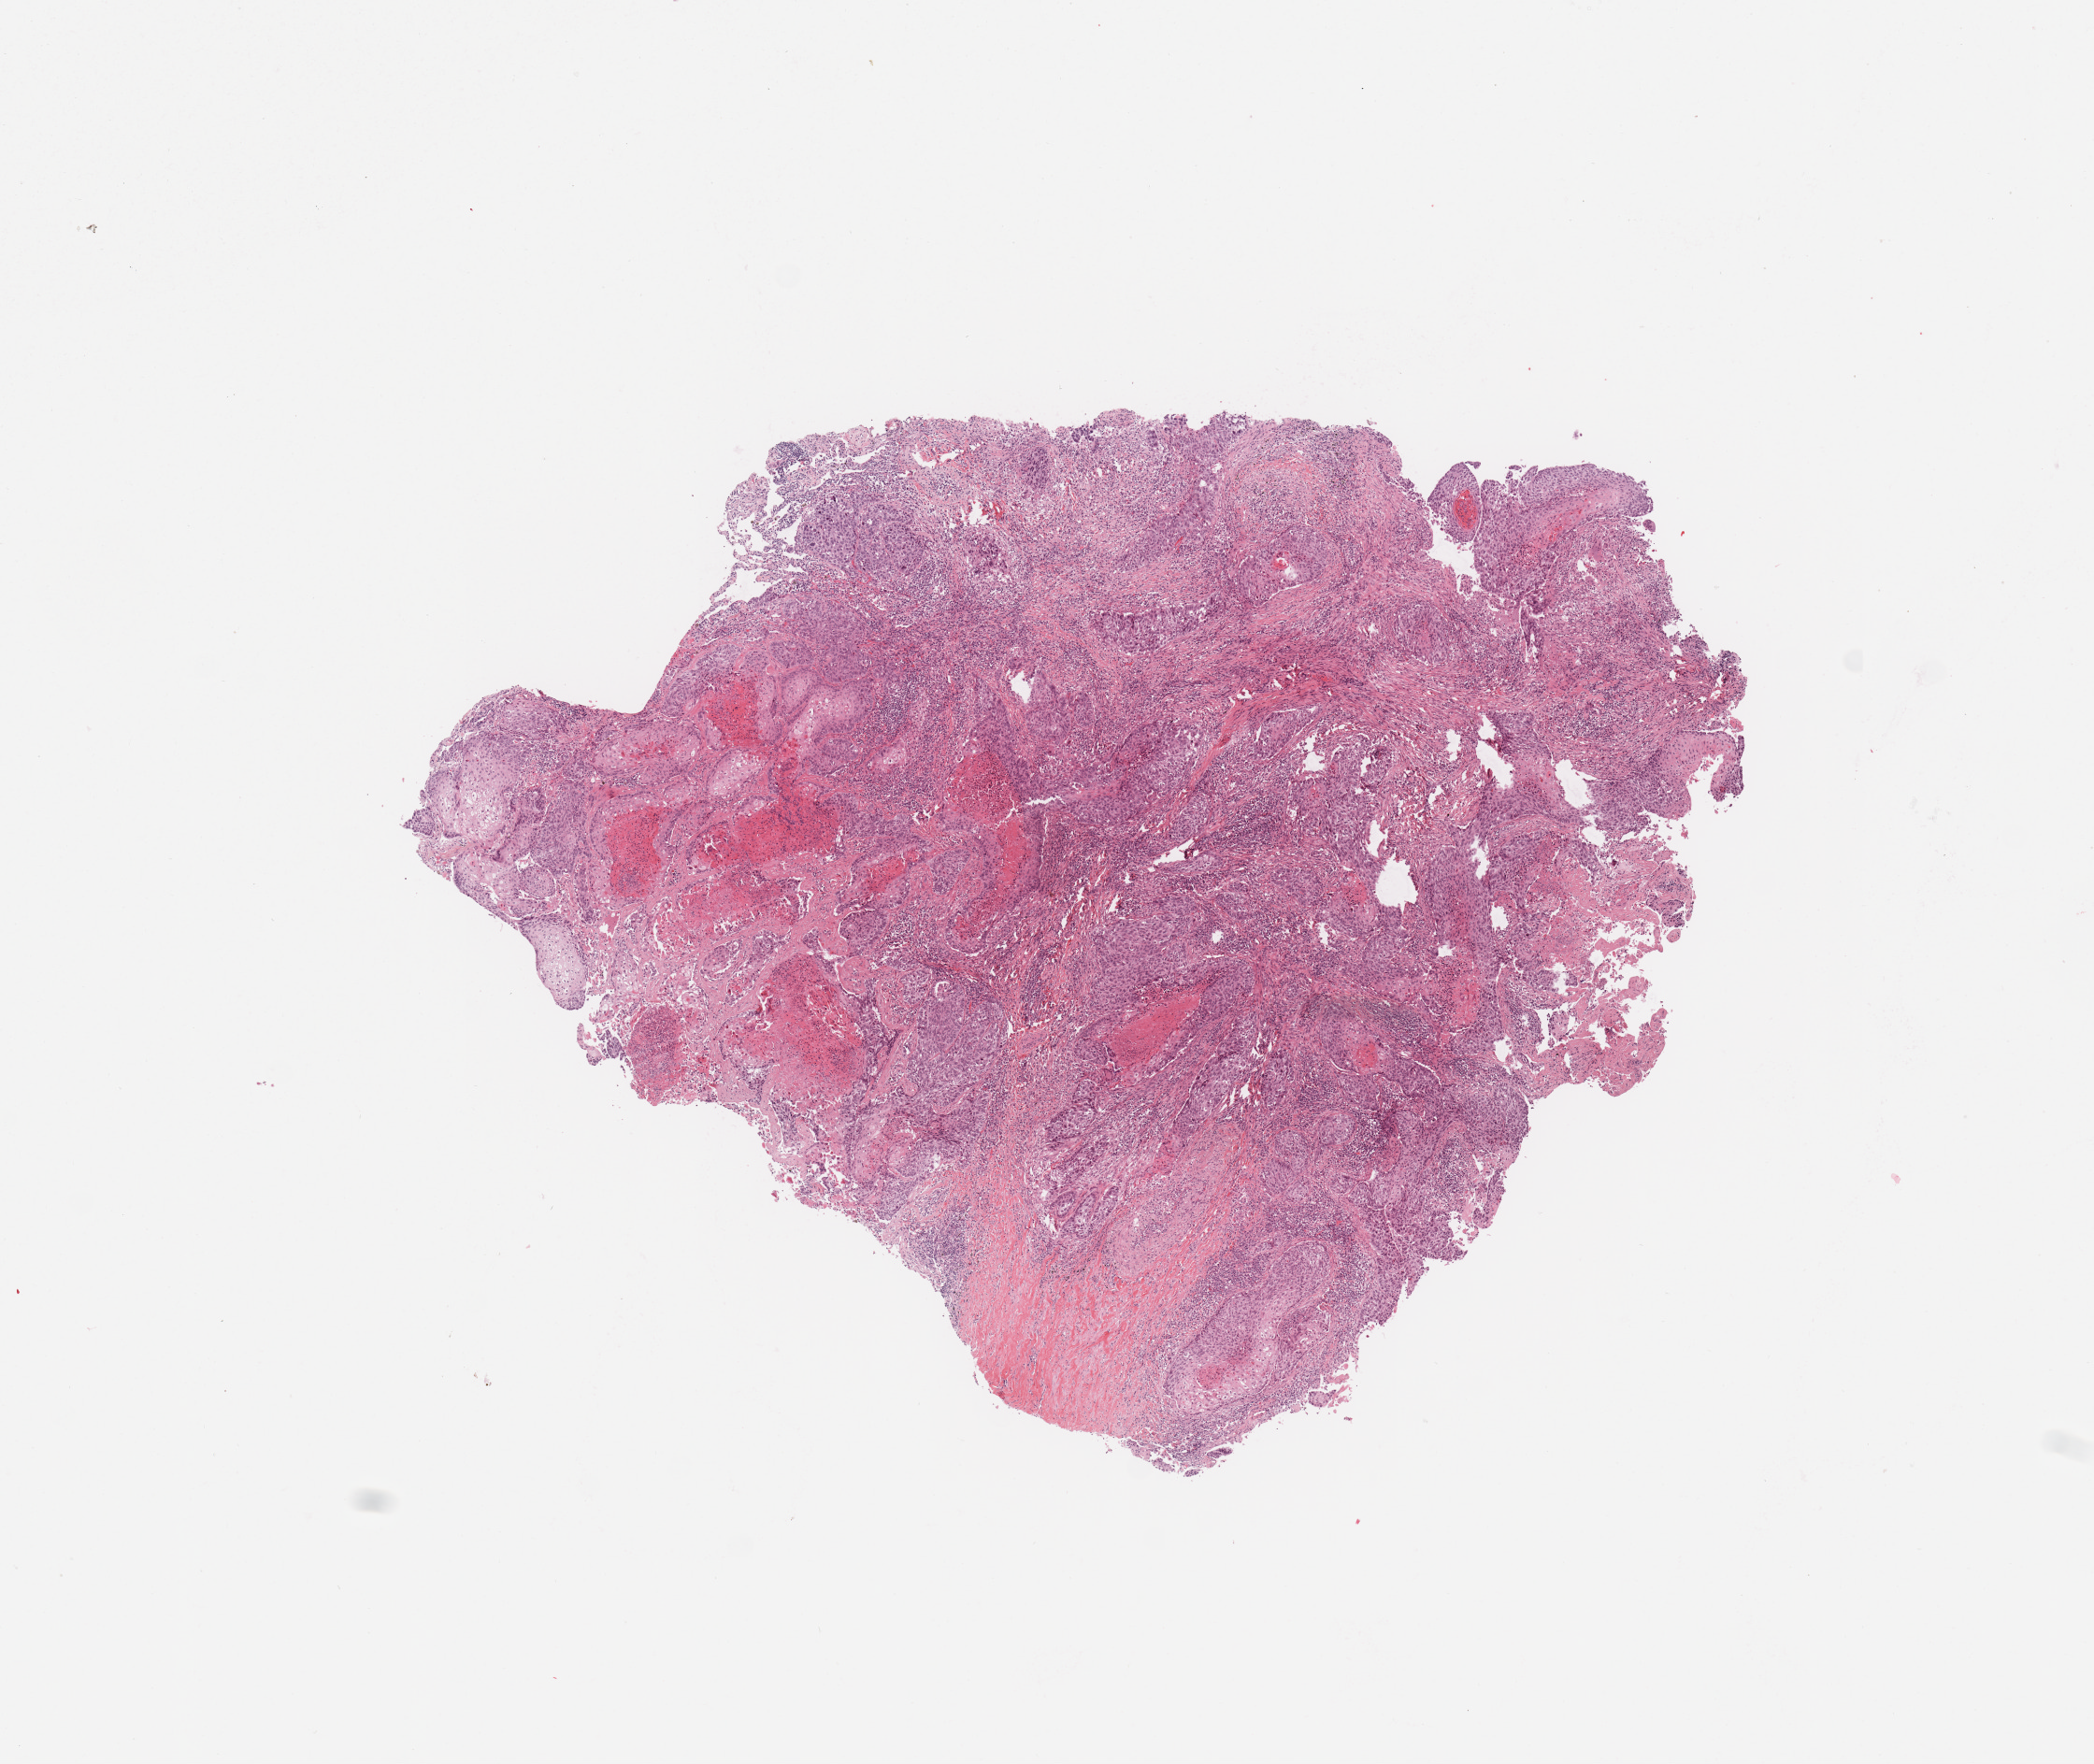
H&E-stained whole-slide image, shown as a low-resolution overview of the whole scanned area (about 8.9 x 7.5 mm, acquisition: 20x scan), tumour tissue sample, sampled site: lung. 62-year-old male patient. Histologic grade: G3 (poorly differentiated). Slide review estimates, as recorded: tumour nuclei 70%, necrosis 10%.
* primary tumour site (as recorded): left upper lobe
* AJCC pathologic stage: IB
* diagnosis: Squamous cell carcinoma, NOS